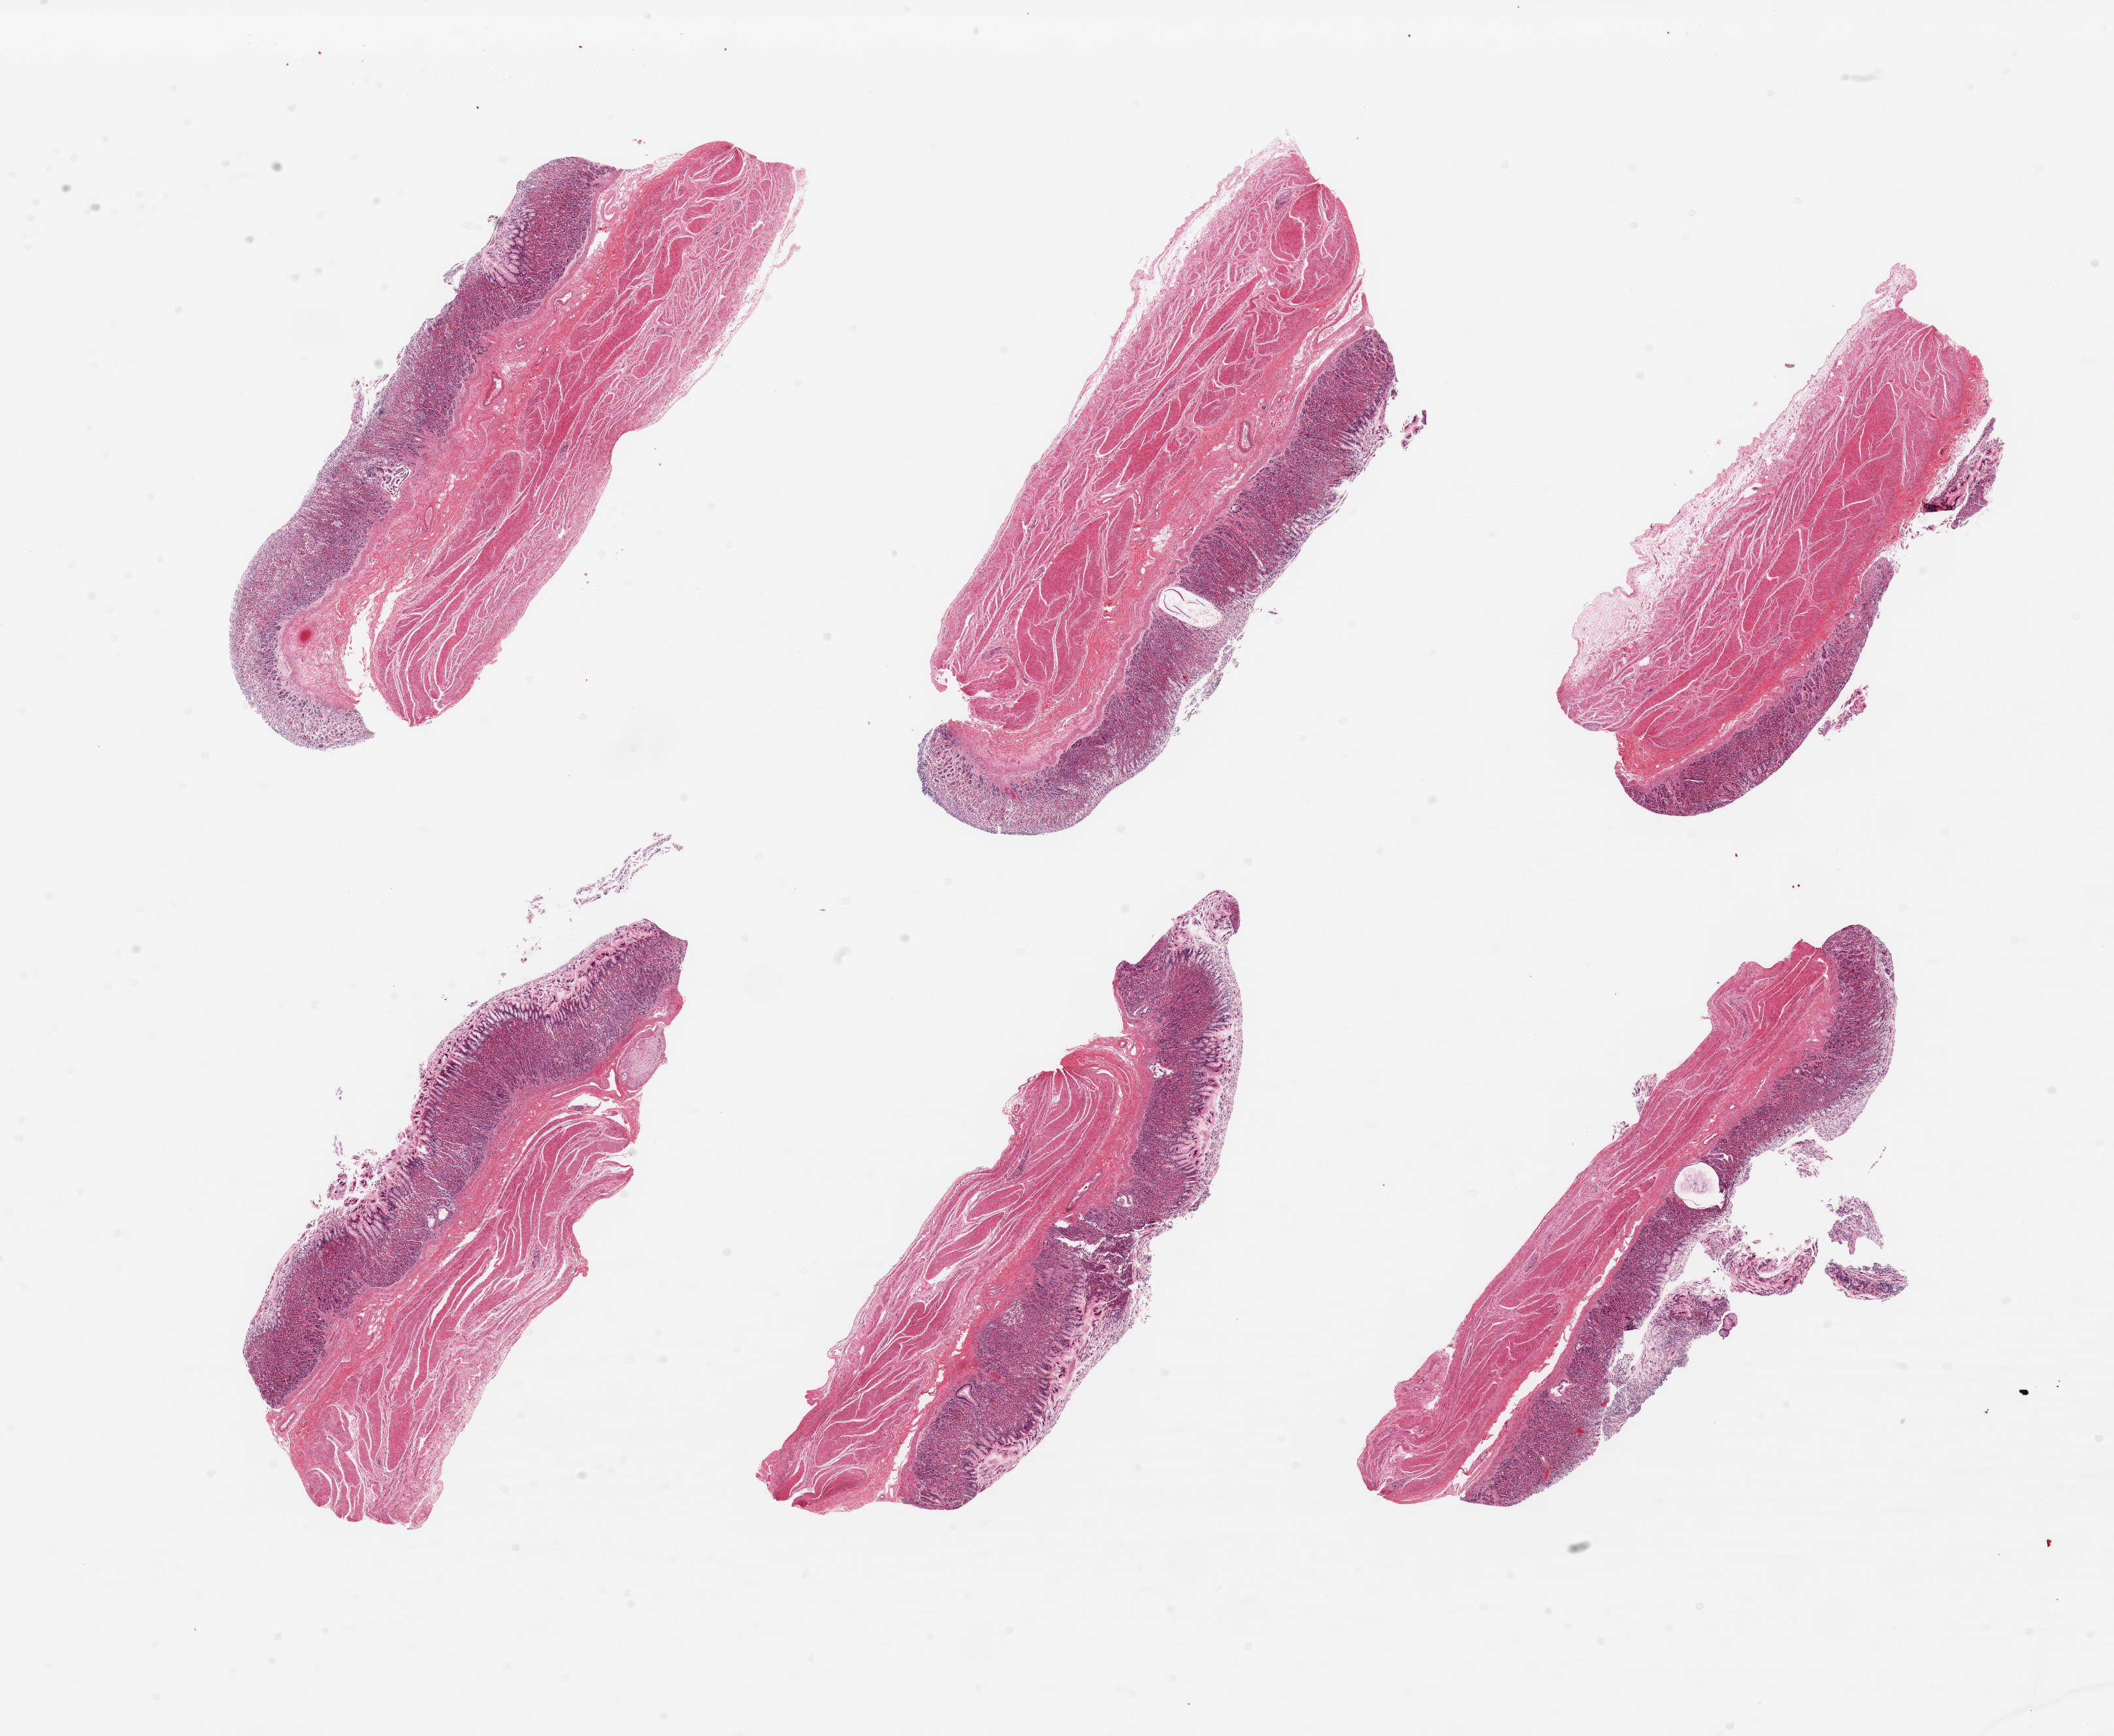
Whole-slide image, H&E stain, a low-resolution overview of the entire scanned area, about 25.6 x 21.0 mm; PAXgene-fixed, paraffin-embedded tissue; target tissue: stomach; donor tissue sample. Donor sex: male.
Reviewer comment on this tissue sample: 6 pieces; mucosal autolysis varies between 2 and 3.